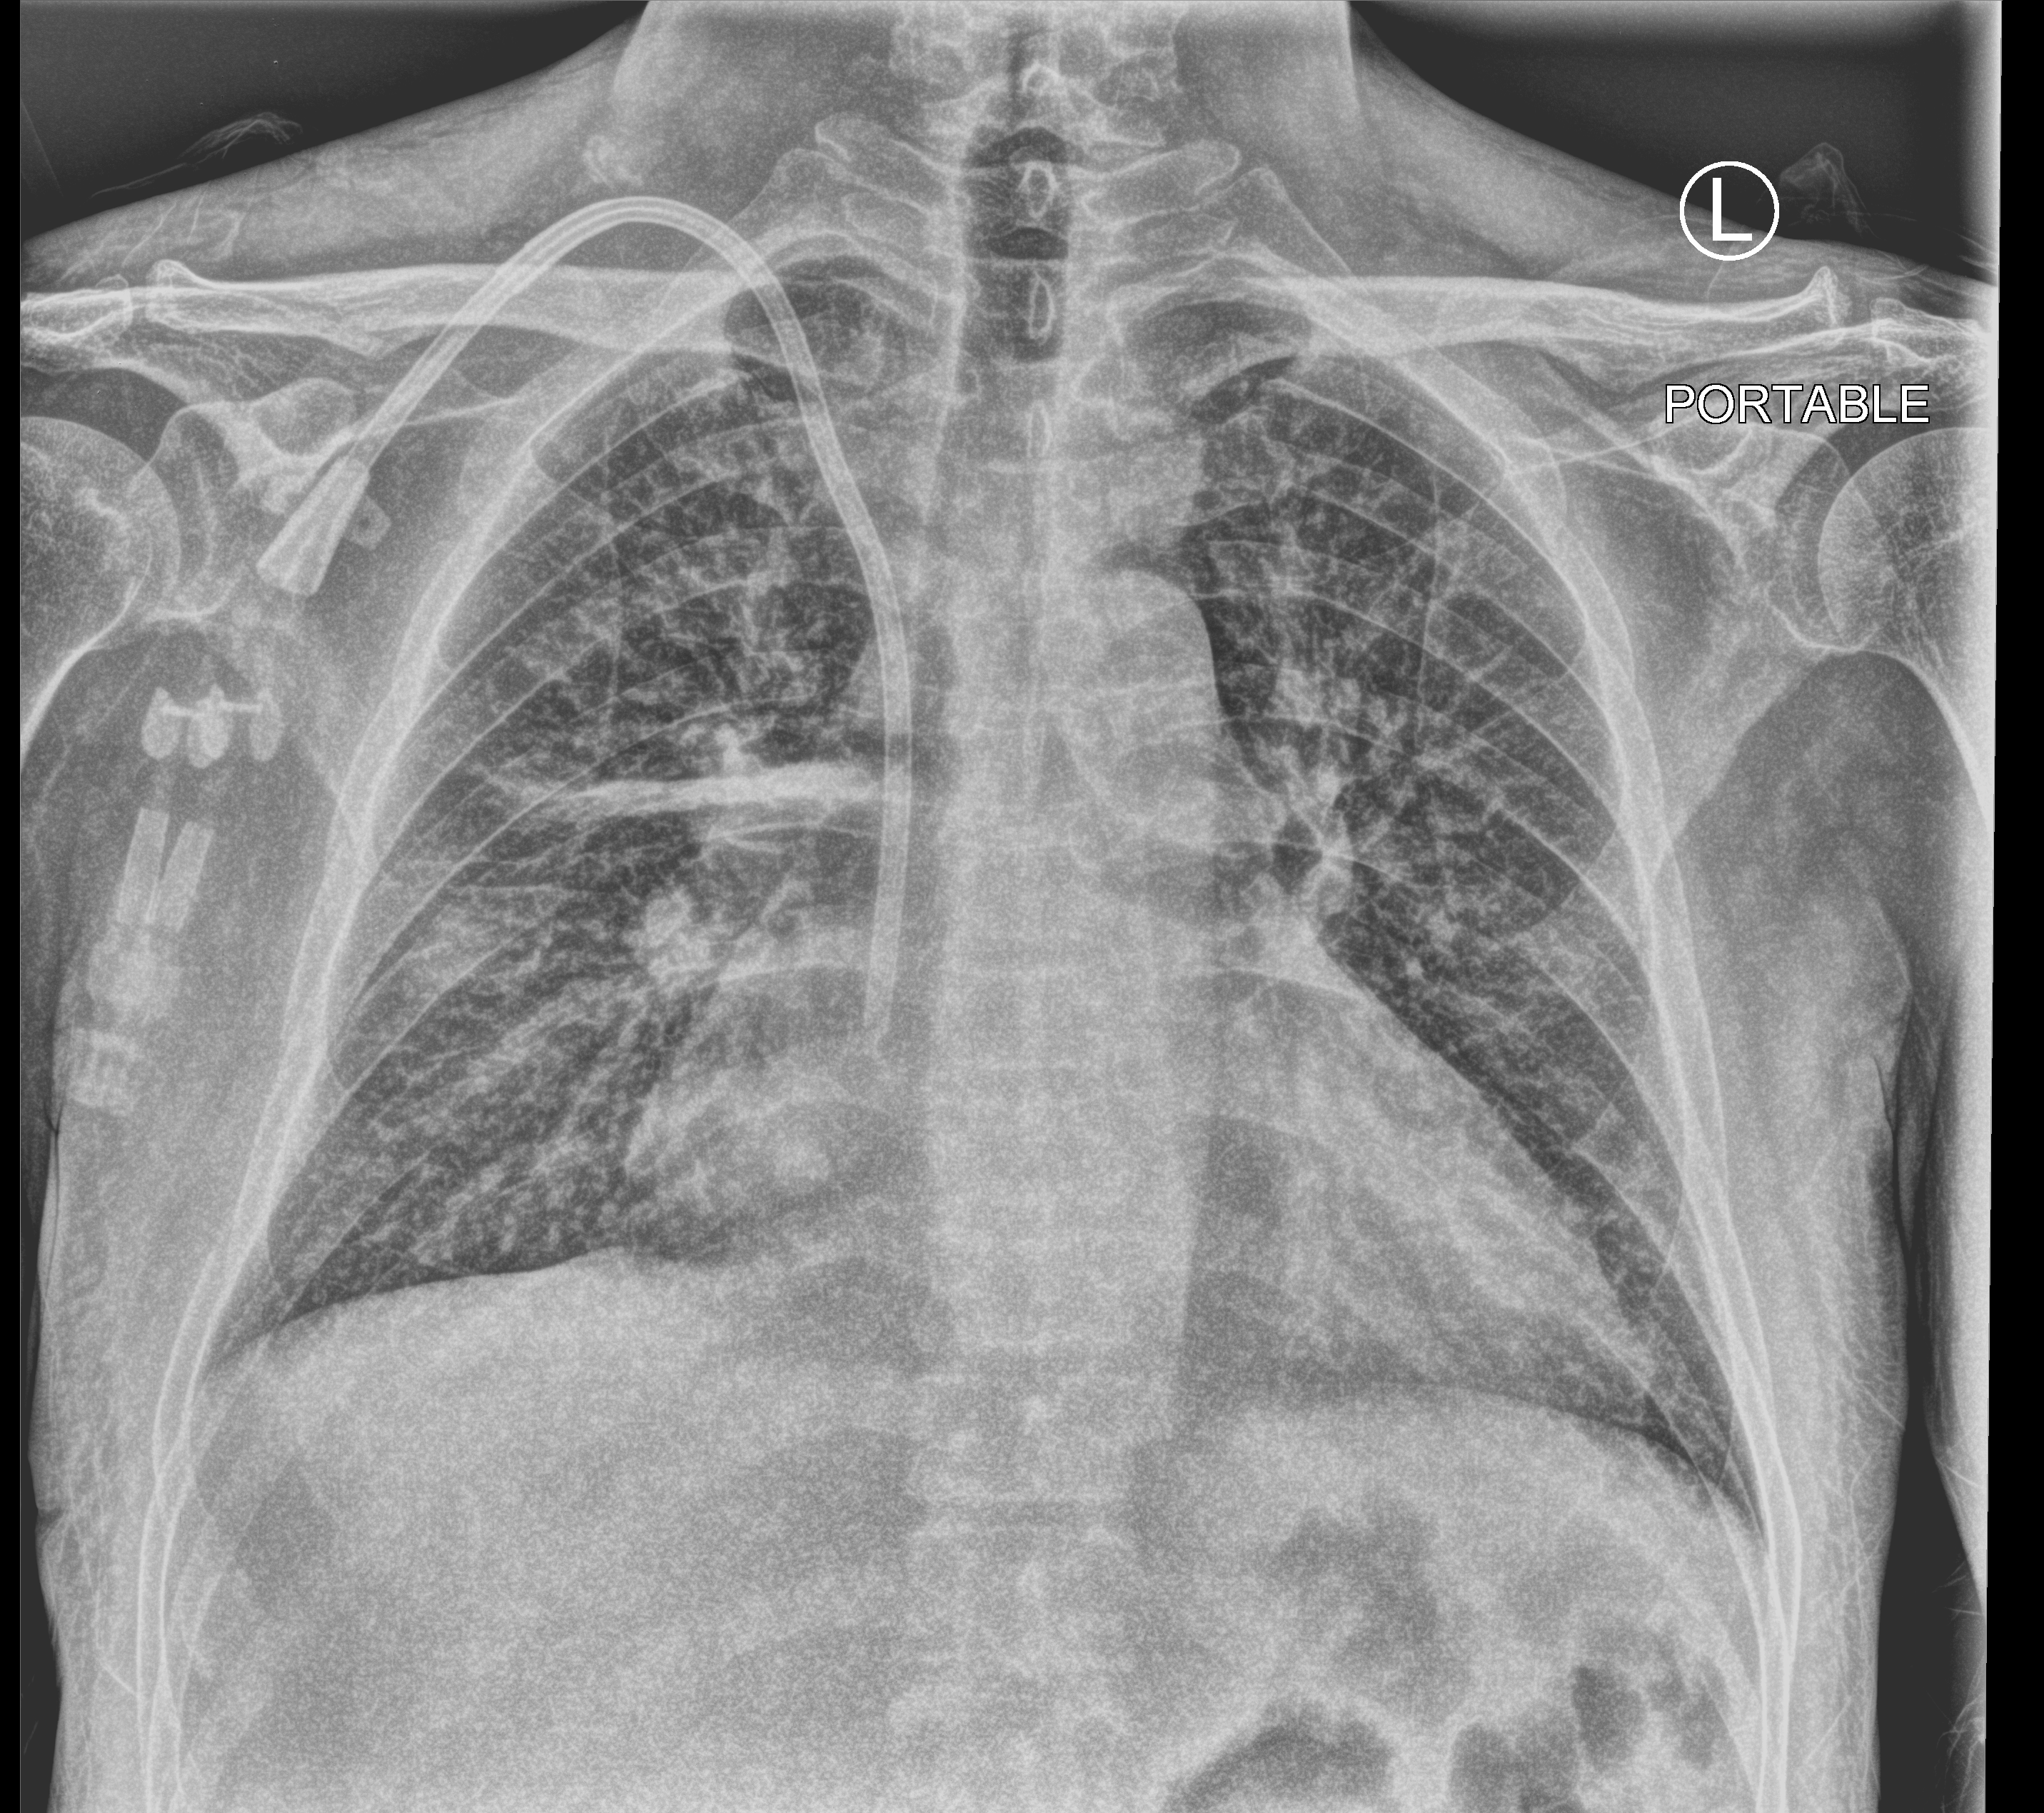
Chest X-ray (portable), anteroposterior (AP) projection. Patient hospitalised with COVID-19; male, aged 18–59 years.
Admission-level facts for this patient (not findings on this image; timing relative to this image not recorded):
- hypertension (admission record): yes
- admitted to intensive care during this hospital stay: no
- mechanically ventilated during this hospital stay: no